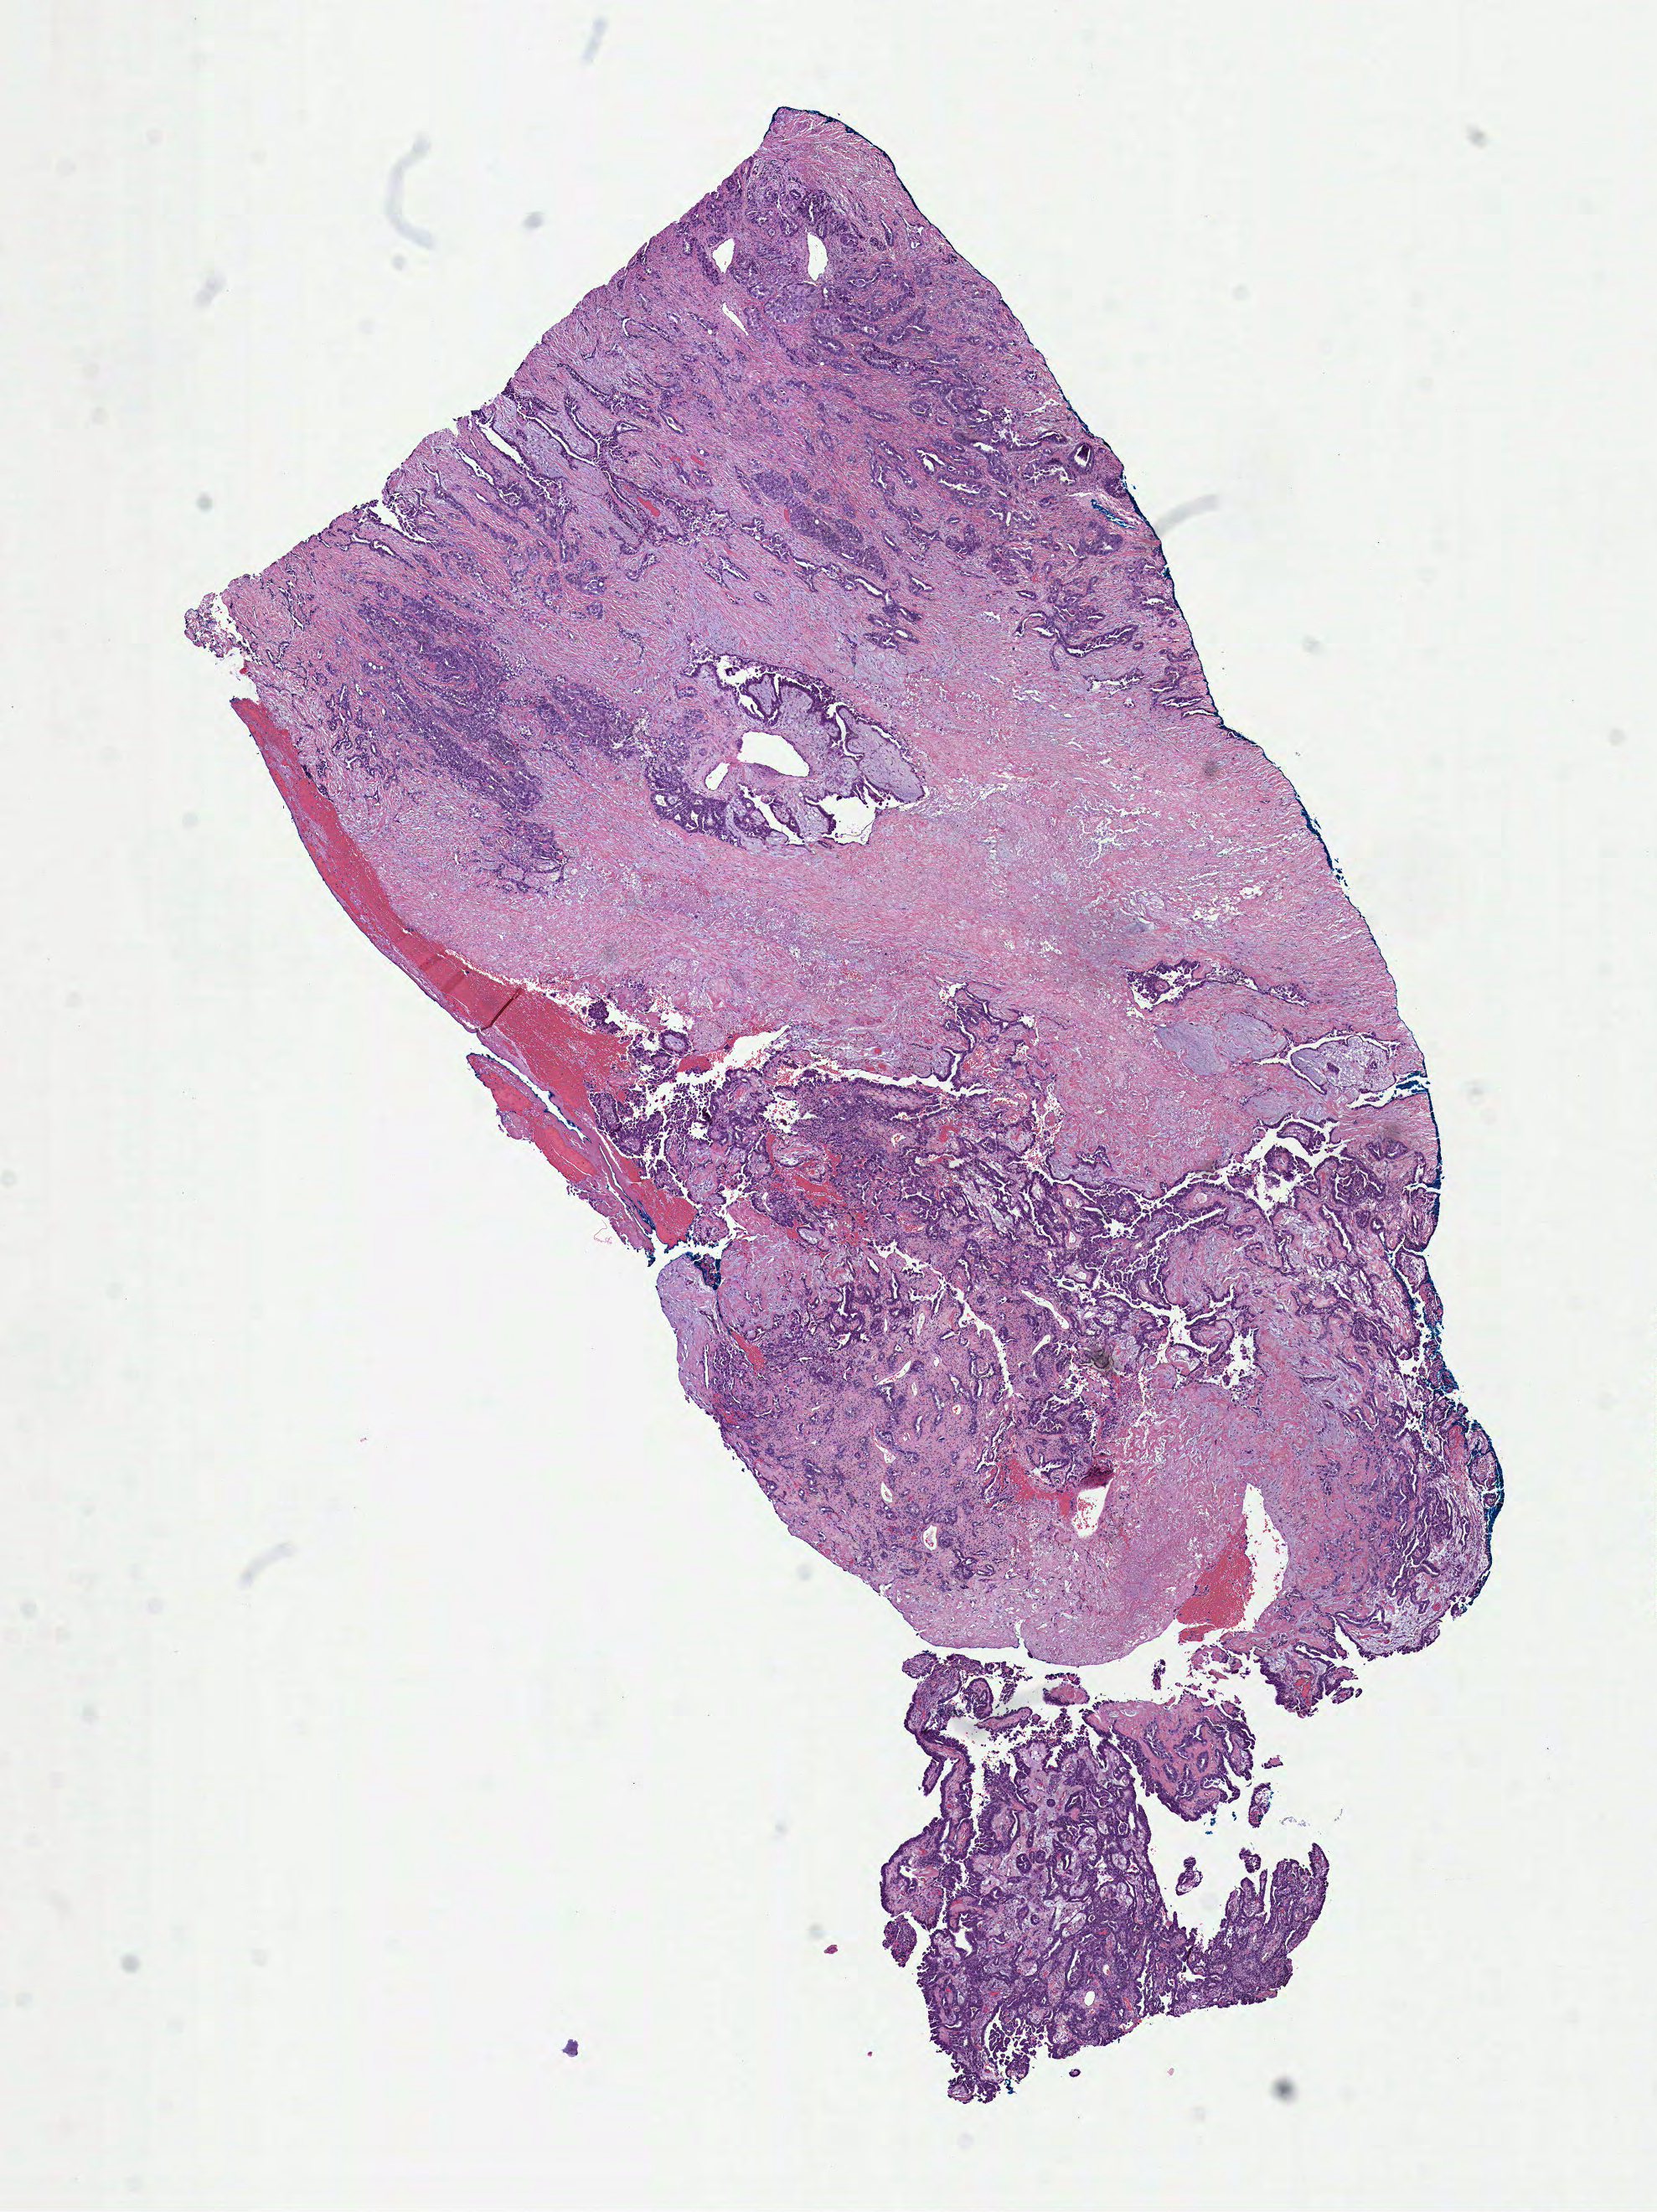
H&E-stained whole-slide image — low-resolution overview of the scanned area, about 8.0 x 10.6 mm (from a 40x scan); FFPE section; sample: primary tumour, ovary. Female patient; age at initial diagnosis 56 years. Histologic grade: G3 (poorly differentiated).
* diagnosis: Serous cystadenocarcinoma, NOS
* FIGO stage: IIIC